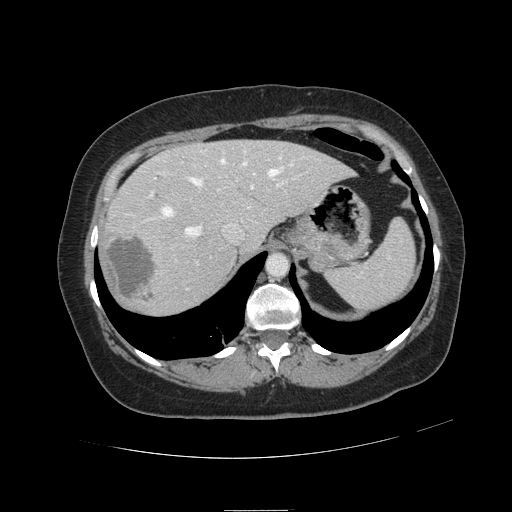
Contrast-enhanced abdominal CT, one axial slice; position 88 of 121 along the scan axis; 120 kVp; soft-tissue window (W 400 / L 40 HU); 2.5 mm slice thickness; 512 × 512 image matrix. Female patient, age 52 years. Case-level facts recorded for this patient, not image findings: diagnosis: colorectal cancer liver metastases, imaged before liver resection; multiple liver metastases: yes; largest metastasis: 6.3 cm; disease in both lobes: no.
Annotated regions visible in this slice (outlined manually by an expert reader):
- hepatic veins: bounding box (x1, y1, x2, y2) in pixels: (158, 152, 292, 236)
- liver: (104, 140, 351, 314)
- planned liver remnant (the part of the liver to remain after resection): (168, 141, 351, 249)
- portal vein (with intrahepatic branches): (149, 181, 286, 289)
- liver metastasis: (105, 234, 155, 303)